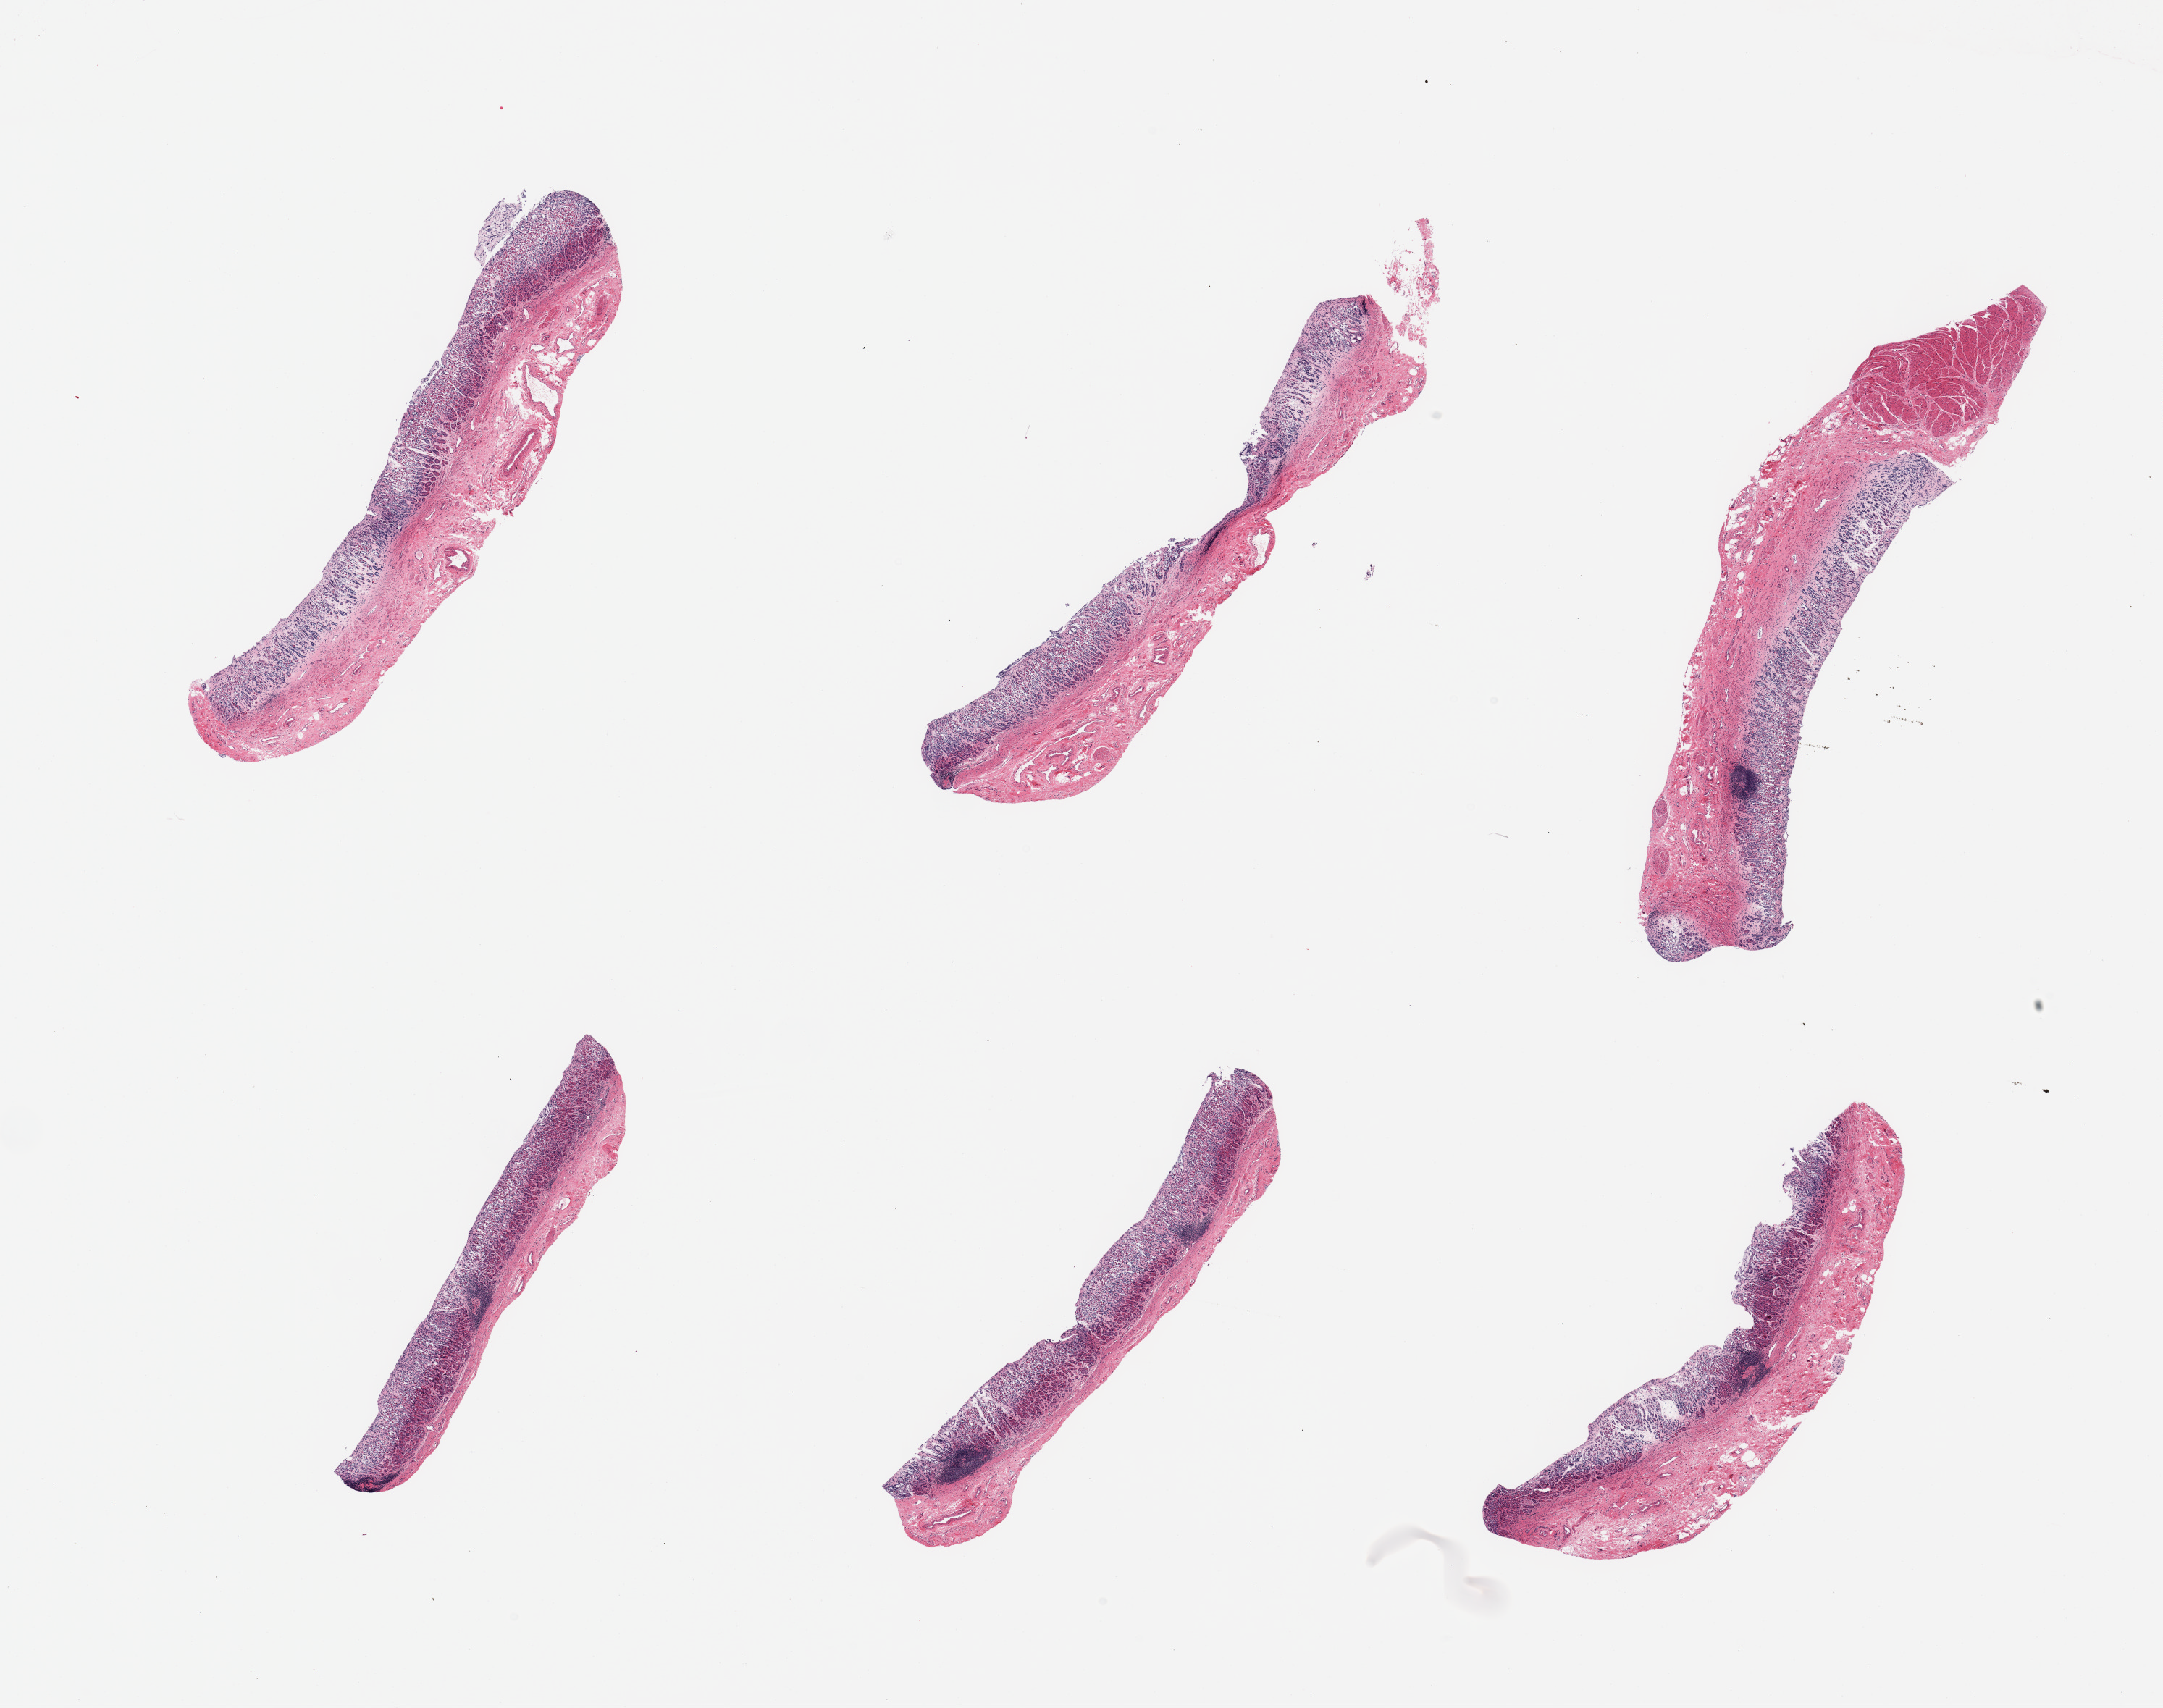
Whole-slide image, haematoxylin and eosin stain, shown as a low-resolution overview of the whole scanned area (about 23.6 x 18.7 mm, acquisition: 20x scan); PAXgene-fixed paraffin-embedded (PFPE) section; section of gastroesophageal junction (target tissue); tissue donor sample.
* review note (as recorded): 6 pieces; all are gastric mucosa, not target